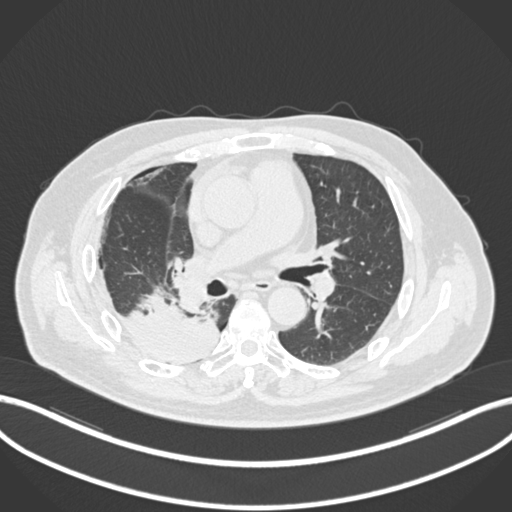
Chest CT, one axial slice. Position 104 of 218 along the scan axis. Reconstruction kernel B30f. Lung window (W 1500 / L -600 HU). 1 mm slice thickness. 512 × 512 image matrix, field of view 400 × 400 mm. Patient: male, 68 years. Case-level facts recorded for this patient, not image findings: clinical TNM (as recorded): T2a N0 M0.
Outlined on this slice (bounding box drawn by a radiologist):
- lung tumour (recorded histology: adenocarcinoma): box from (x=116, y=285) to (x=219, y=370) px